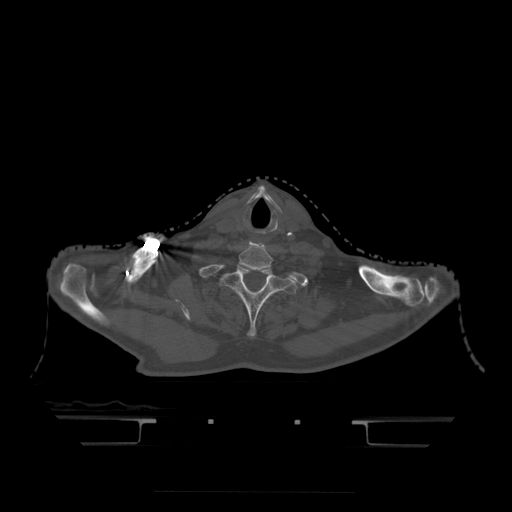
CT including the spine, one axial slice. Slice 401 of 522 in the series (ordered by position). Bone window (W 1800 / L 400 HU). 512 × 512 image matrix, field of view 436 × 436 mm. Patient age 68 years. From the clinical record (not read from this slice): primary cancer: urothelial.
Annotated regions visible in this slice (semi-automatic segmentation, software-assisted and operator-edited):
- T1 vertebra: box from (x=222, y=265) to (x=298, y=336) px